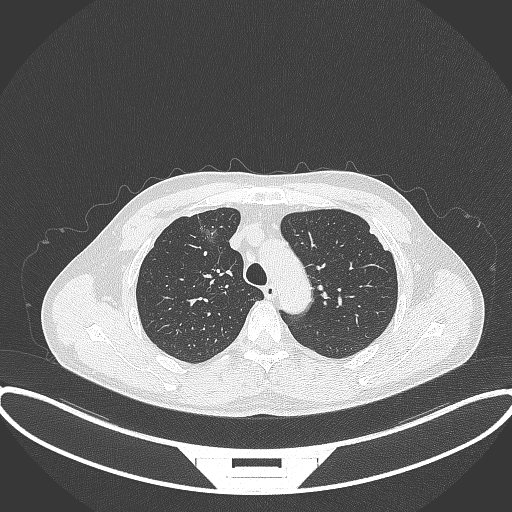
Chest CT, one axial slice. Reconstruction kernel B70f. 120 kVp. Lung window (W 1500 / L -600 HU). 1 mm slice thickness. 512 × 512 image matrix, field of view 424 × 424 mm. Patient: male, 60 years. Case-level facts recorded for this patient, not image findings: clinical TNM (as recorded): T1c N0 M0.
Annotated regions visible in this slice (bounding box drawn by a radiologist):
- lung tumour (recorded histology: adenocarcinoma): bounding box <191,215,225,253> (left, top, right, bottom; pixels)